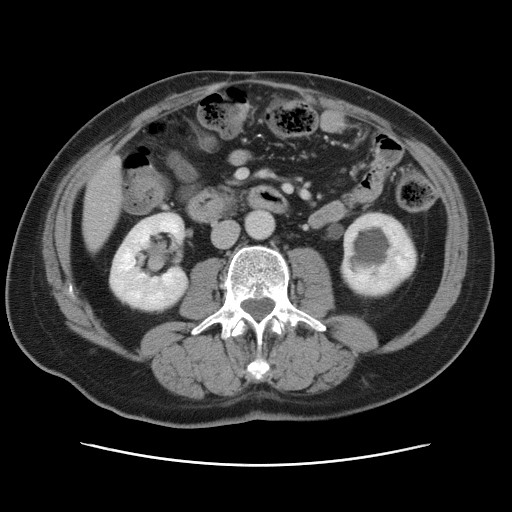
Contrast-enhanced abdominal CT, one axial slice; position 17 of 80 along the scan axis; 120 kVp; intravenous contrast given; soft-tissue window (W 400 / L 40 HU); 5 mm slice thickness; 512 × 512 image matrix, field of view 370 × 370 mm. Male patient, age 69 years. Case-level facts recorded for this patient, not image findings: diagnosis: colorectal cancer liver metastases, imaged before liver resection; multiple liver metastases: no; largest metastasis: 5 cm; disease in both lobes: yes.
Structures marked on this image (outlined manually by an expert reader):
- liver: bounding box <84,159,122,249> (left, top, right, bottom; pixels)
- planned liver remnant (the part of the liver to remain after resection): <84,226,110,250>